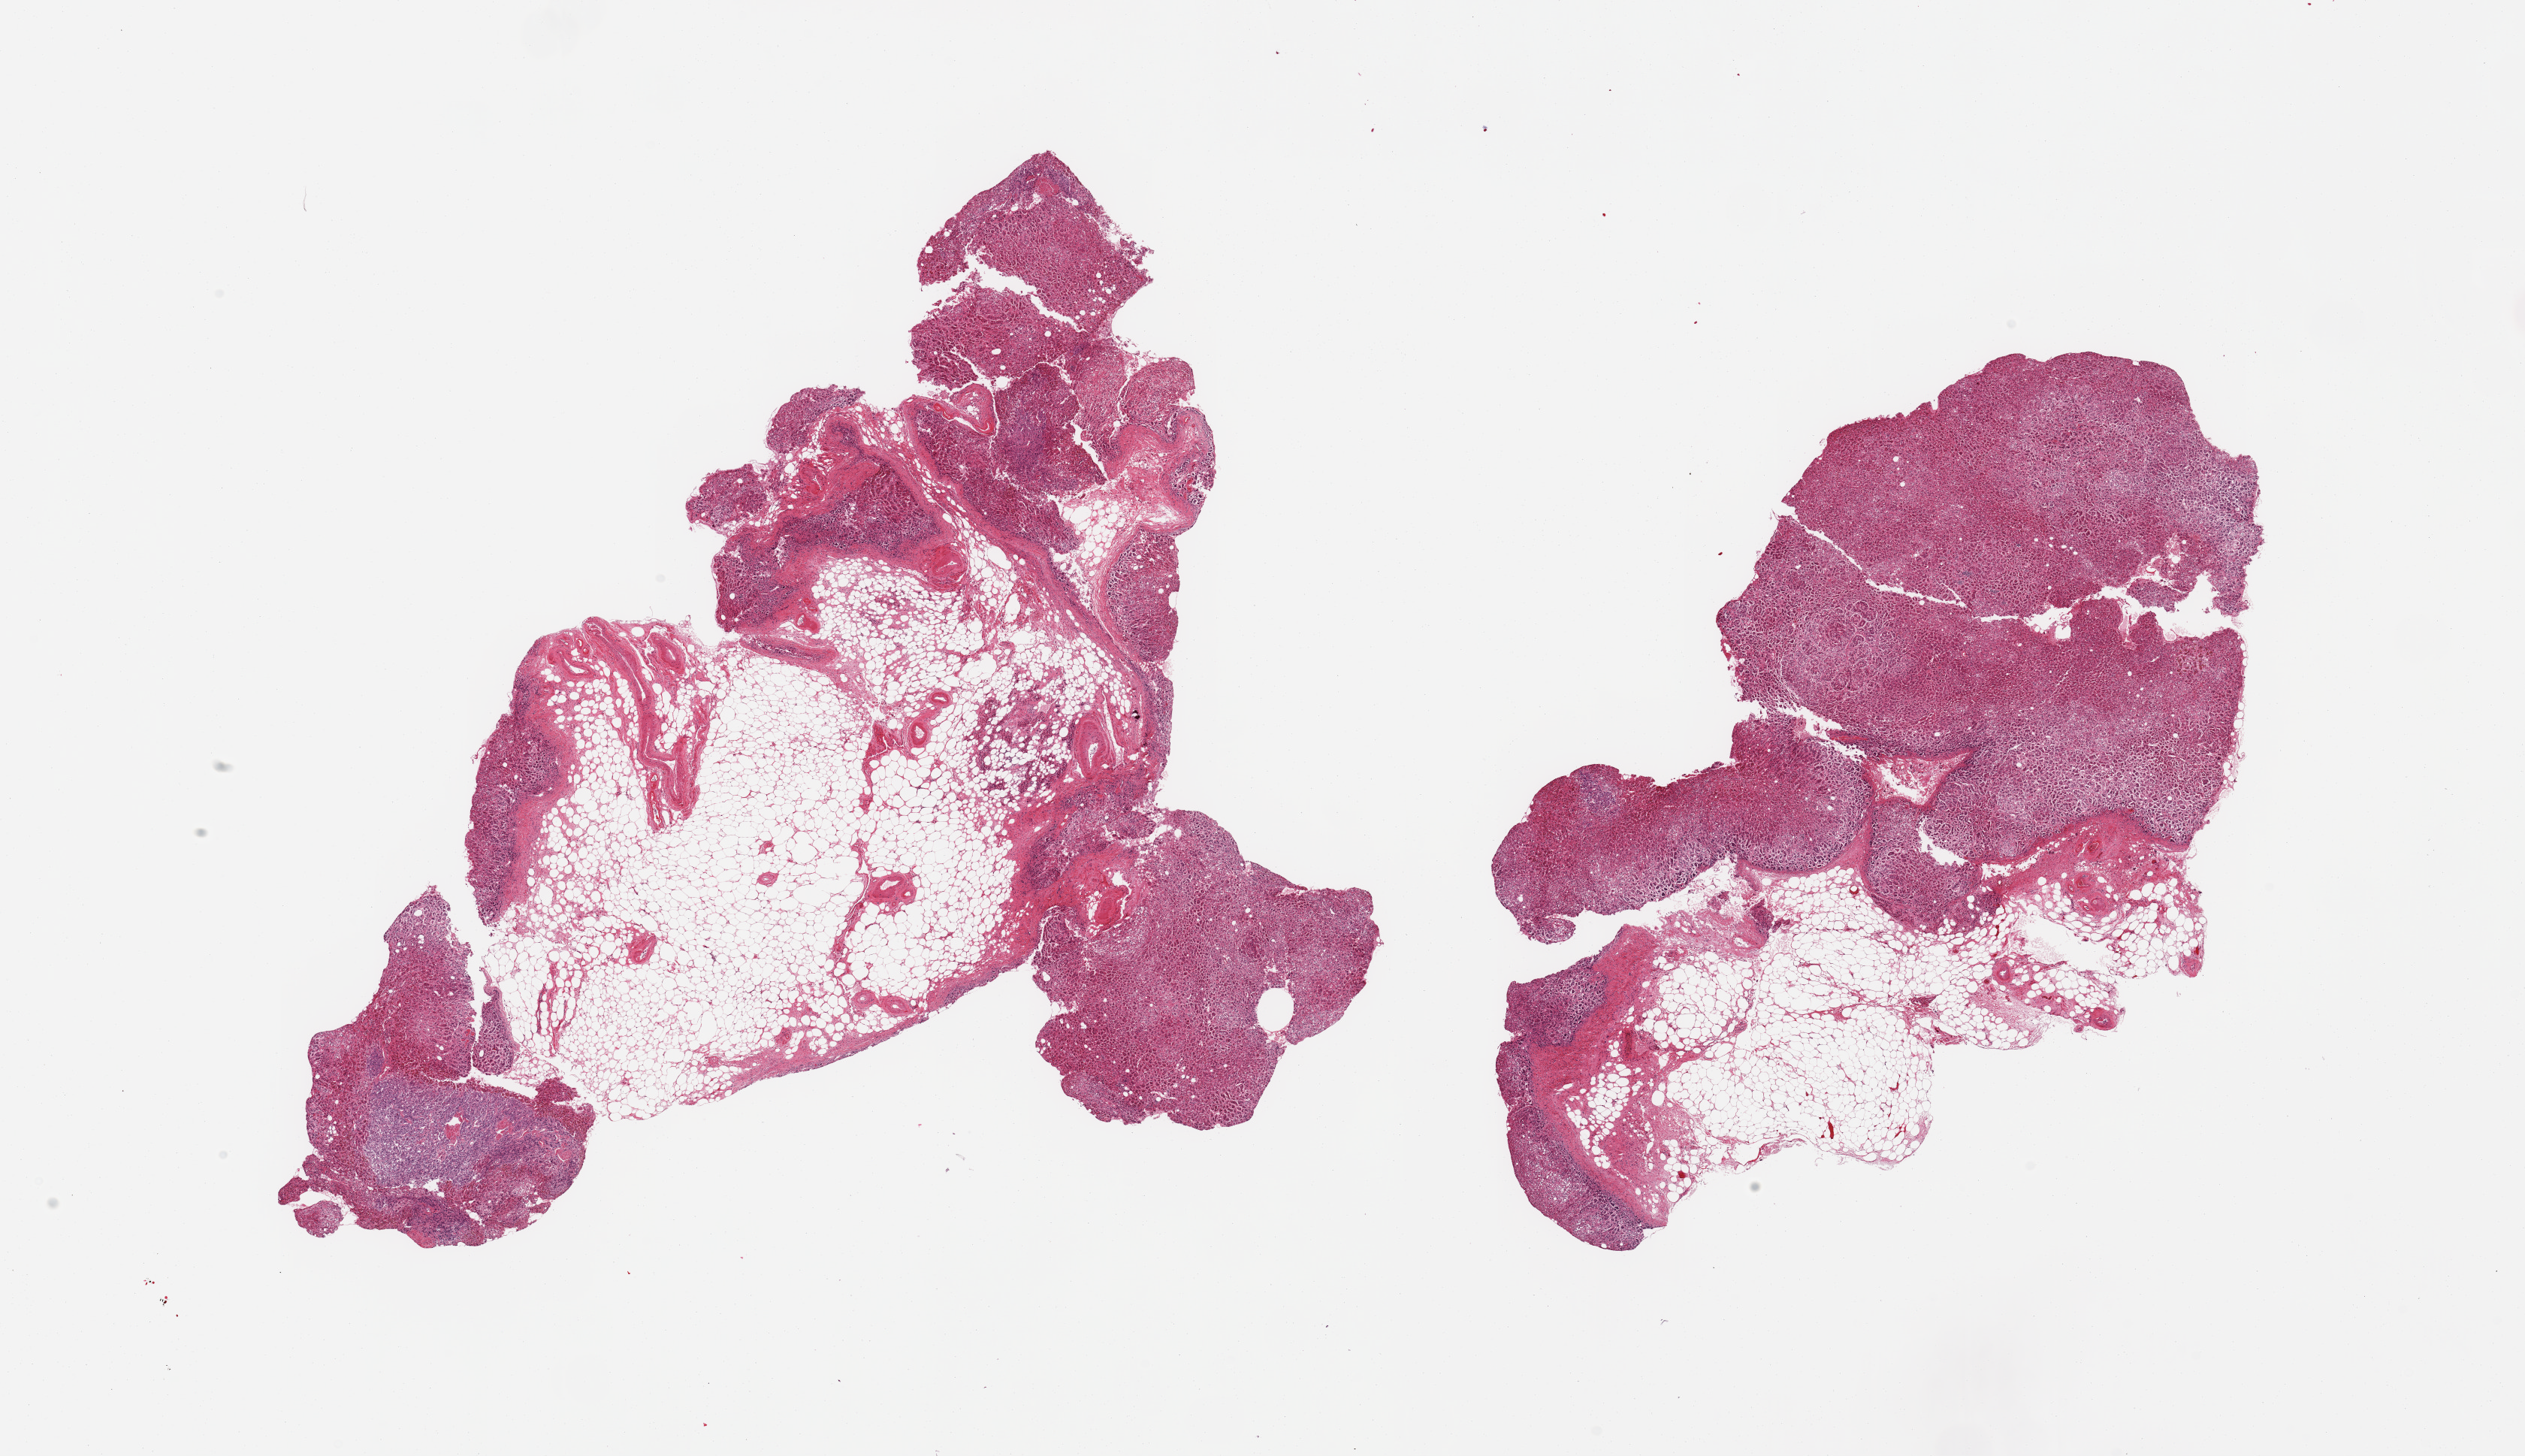
Digitized H&E-stained section, brightfield, low-resolution overview of the scanned area, about 26.6 x 15.3 mm (from a 20x scan). PAXgene-fixed, paraffin-embedded tissue. Sampled site (target tissue): adrenal gland. Tissue donor sample.
Pathologist's review note for this sample: 2 pieces, cortex, ~40% interstitial/adherent fat.